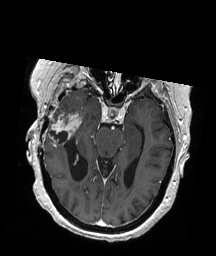
Brain MRI from a brain-tumour surgery series, one axial slice. Position 120 of 192 along the scan axis. T1-weighted post-contrast. 216 × 256 image matrix, field of view 211 × 250 mm. From the clinical record (not read from this slice): histopathology: Glioblastoma; WHO grade: 4; IDH mutation: no; tumour location: Right Temporal.
Annotated regions visible in this slice (outlined manually by an expert reader):
- tumour: bounding box <49,113,82,137> (left, top, right, bottom; pixels)